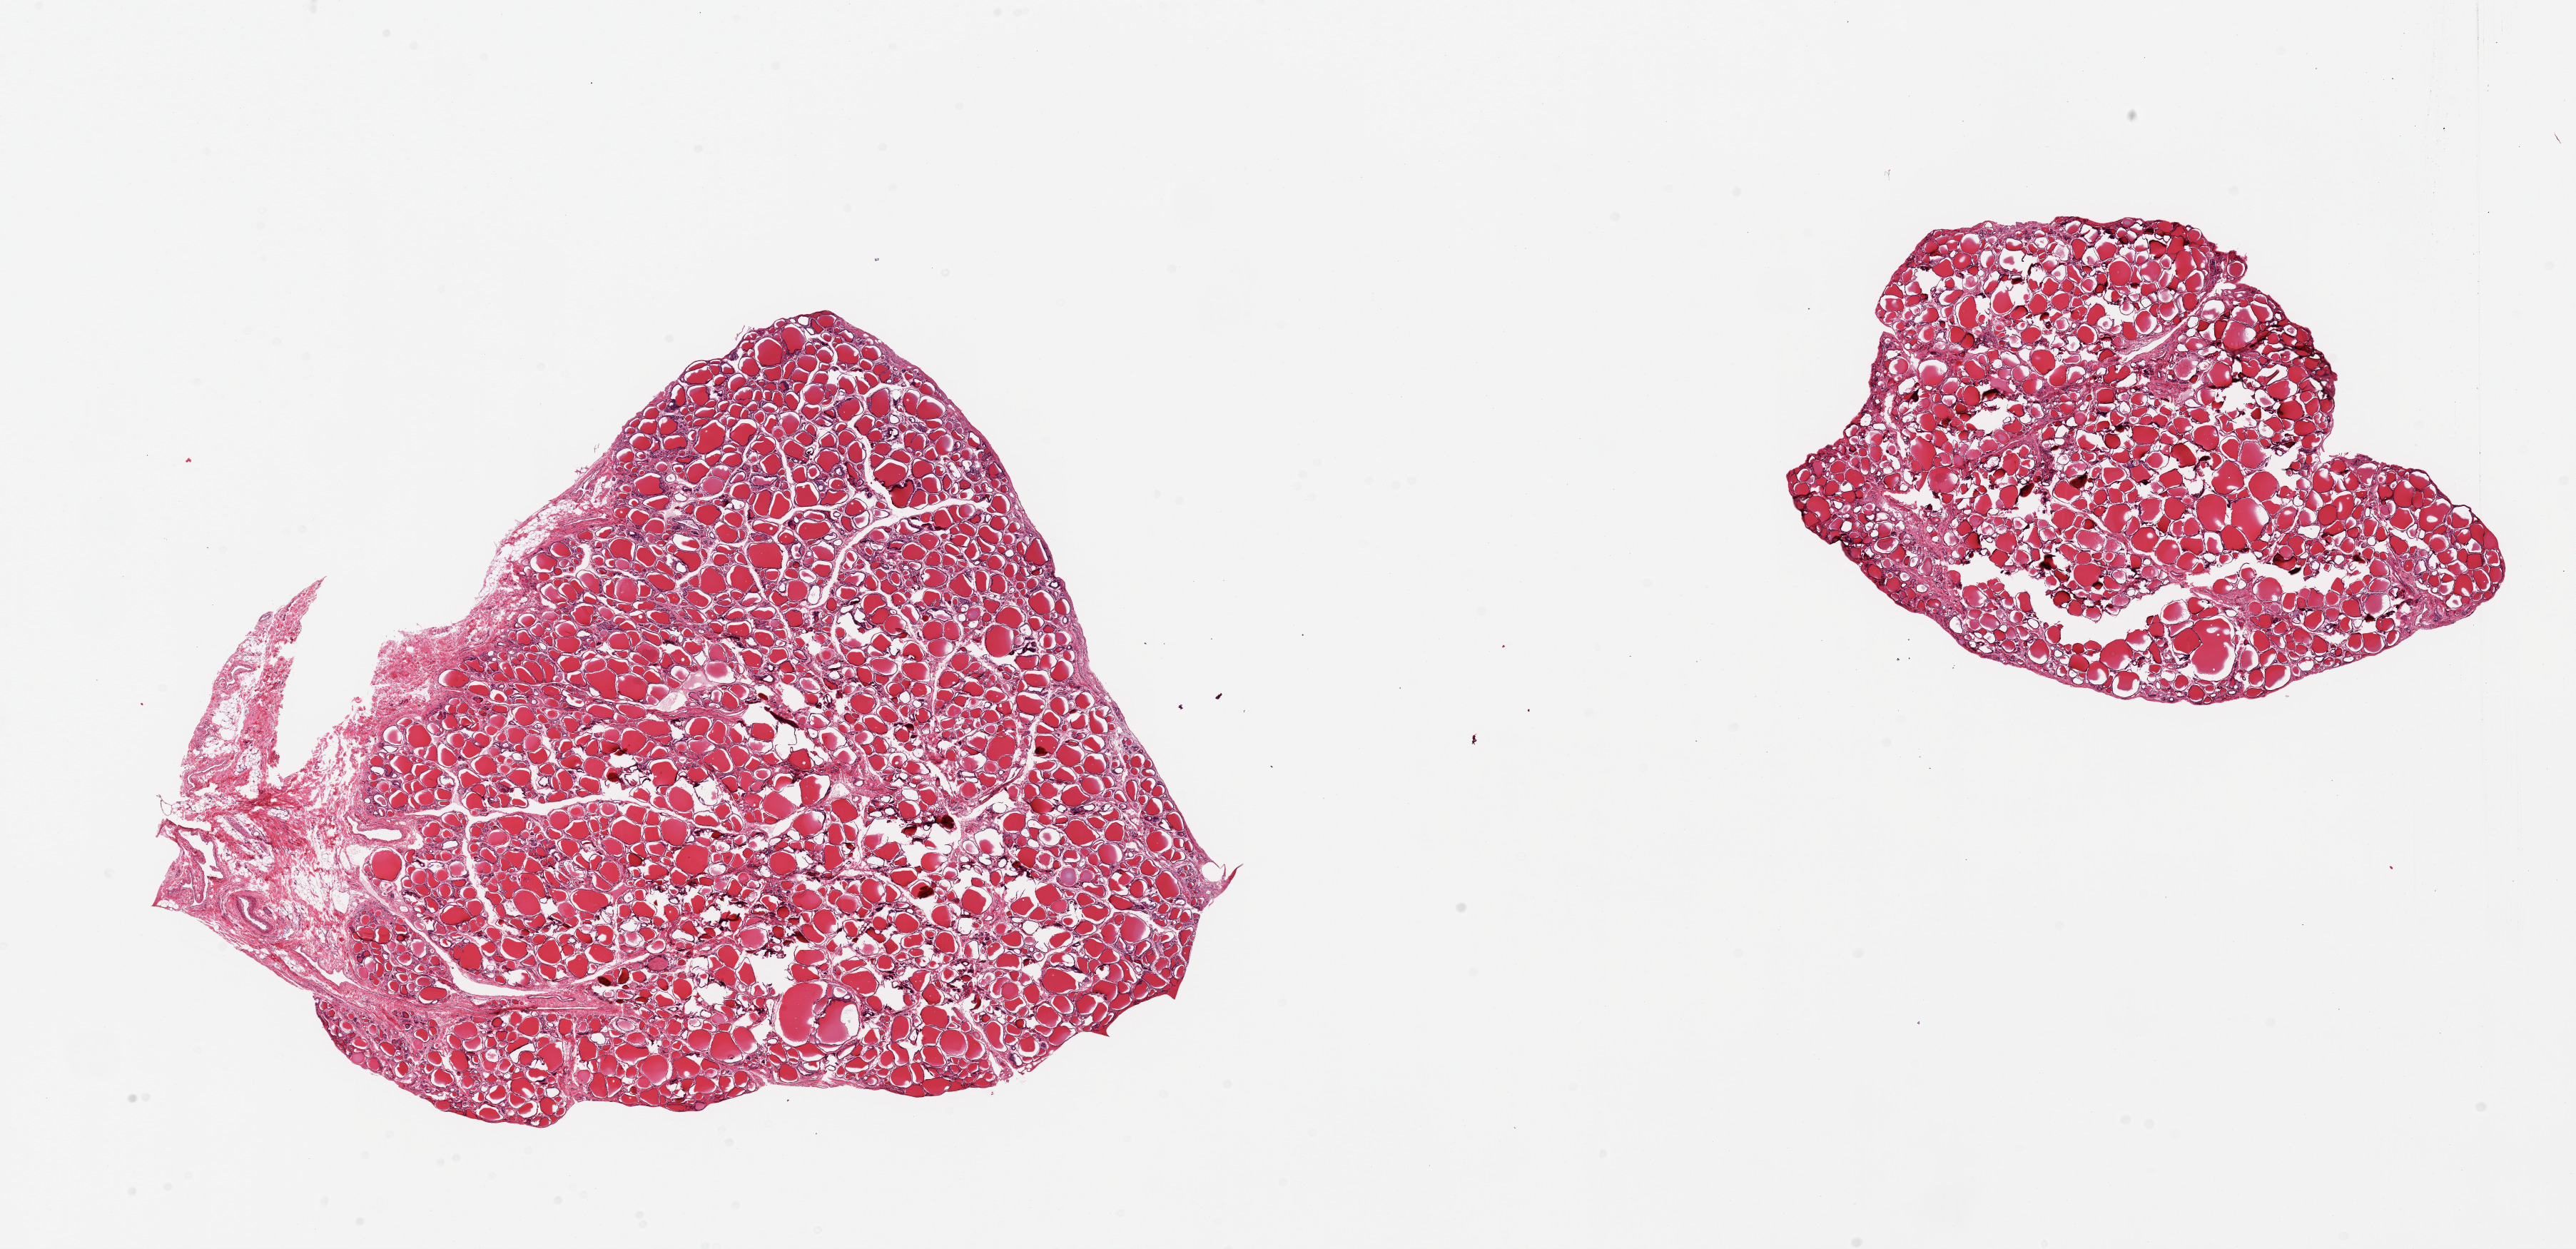
Digitized H&E-stained section, whole scanned area (about 28.5 x 13.8 mm) shown as a low-resolution overview, PAXgene-fixed paraffin-embedded (PFPE) section, sampled site (target tissue): thyroid, donor tissue sample.
Review note (as recorded): 2 pieces.